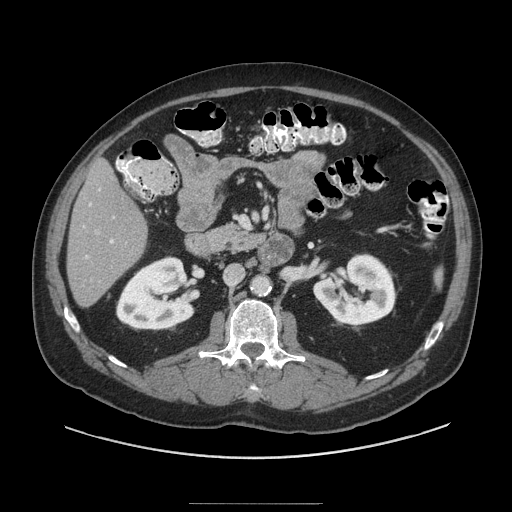
Contrast-enhanced abdominal CT (liver protocol), one axial slice; slice 36 of 91 in the series (ordered by position); soft-tissue window (W 400 / L 40 HU); 512 × 512 image matrix, field of view 440 × 440 mm. Case-level facts recorded for this patient, not image findings: diagnosis: hepatocellular carcinoma (patient treated with transarterial chemoembolisation; whether this scan precedes or follows treatment is not stated here); TNM stage (as recorded): Stage-I; Child-Pugh class: A; tumour differentiation: well differentiated; tumour size: 4 cm.
Outlined on this slice (semi-automatically segmented with operator editing):
- liver parenchyma outside the tumour (the mass and vessels are separate outlines, so this box may not span the whole liver): box from (x=66, y=160) to (x=146, y=306) px
- liver vessels: (x=85, y=189)–(x=114, y=259)